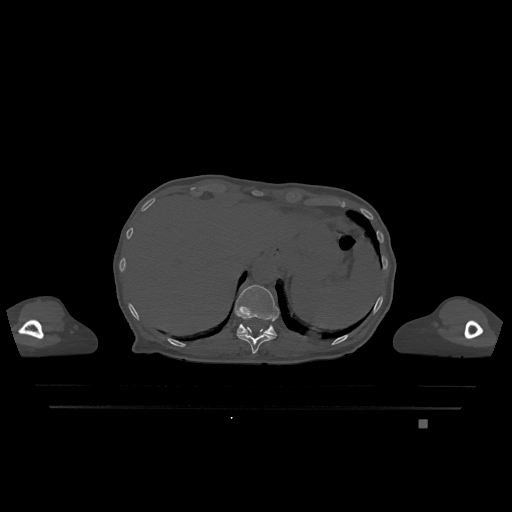
CT including the spine, one axial slice; slice 563 of 1317 in the series (ordered by position); bone window (W 1800 / L 400 HU); 0.5 mm slice thickness; 512 × 512 image matrix. Patient: female, 74 years. From the clinical record (not read from this slice): primary cancer: lung; vertebrae with lytic lesions (as recorded): T1, T4, T5, T6, L4, L5.
Structures marked on this image (semi-automatically segmented with operator editing):
- T11 vertebra: bounding box [x1, y1, x2, y2] px = [237, 327, 276, 354]
- T12 vertebra: [235, 285, 279, 336]